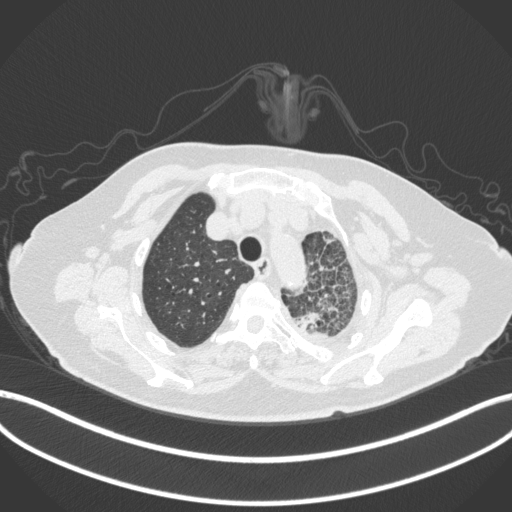
Chest CT, one axial slice; position 323 of 399 along the scan axis; lung window (W 1500 / L -600 HU); 512 × 512 image matrix, field of view 400 × 400 mm. Female patient, age 75 years. From the clinical record (not read from this slice): clinical TNM (as recorded): T3 N3 M1.
Annotated regions visible in this slice (rectangle marked by the reading radiologist):
- lung tumour (recorded histology: adenocarcinoma): bounding box [x1, y1, x2, y2] px = [289, 308, 333, 344]